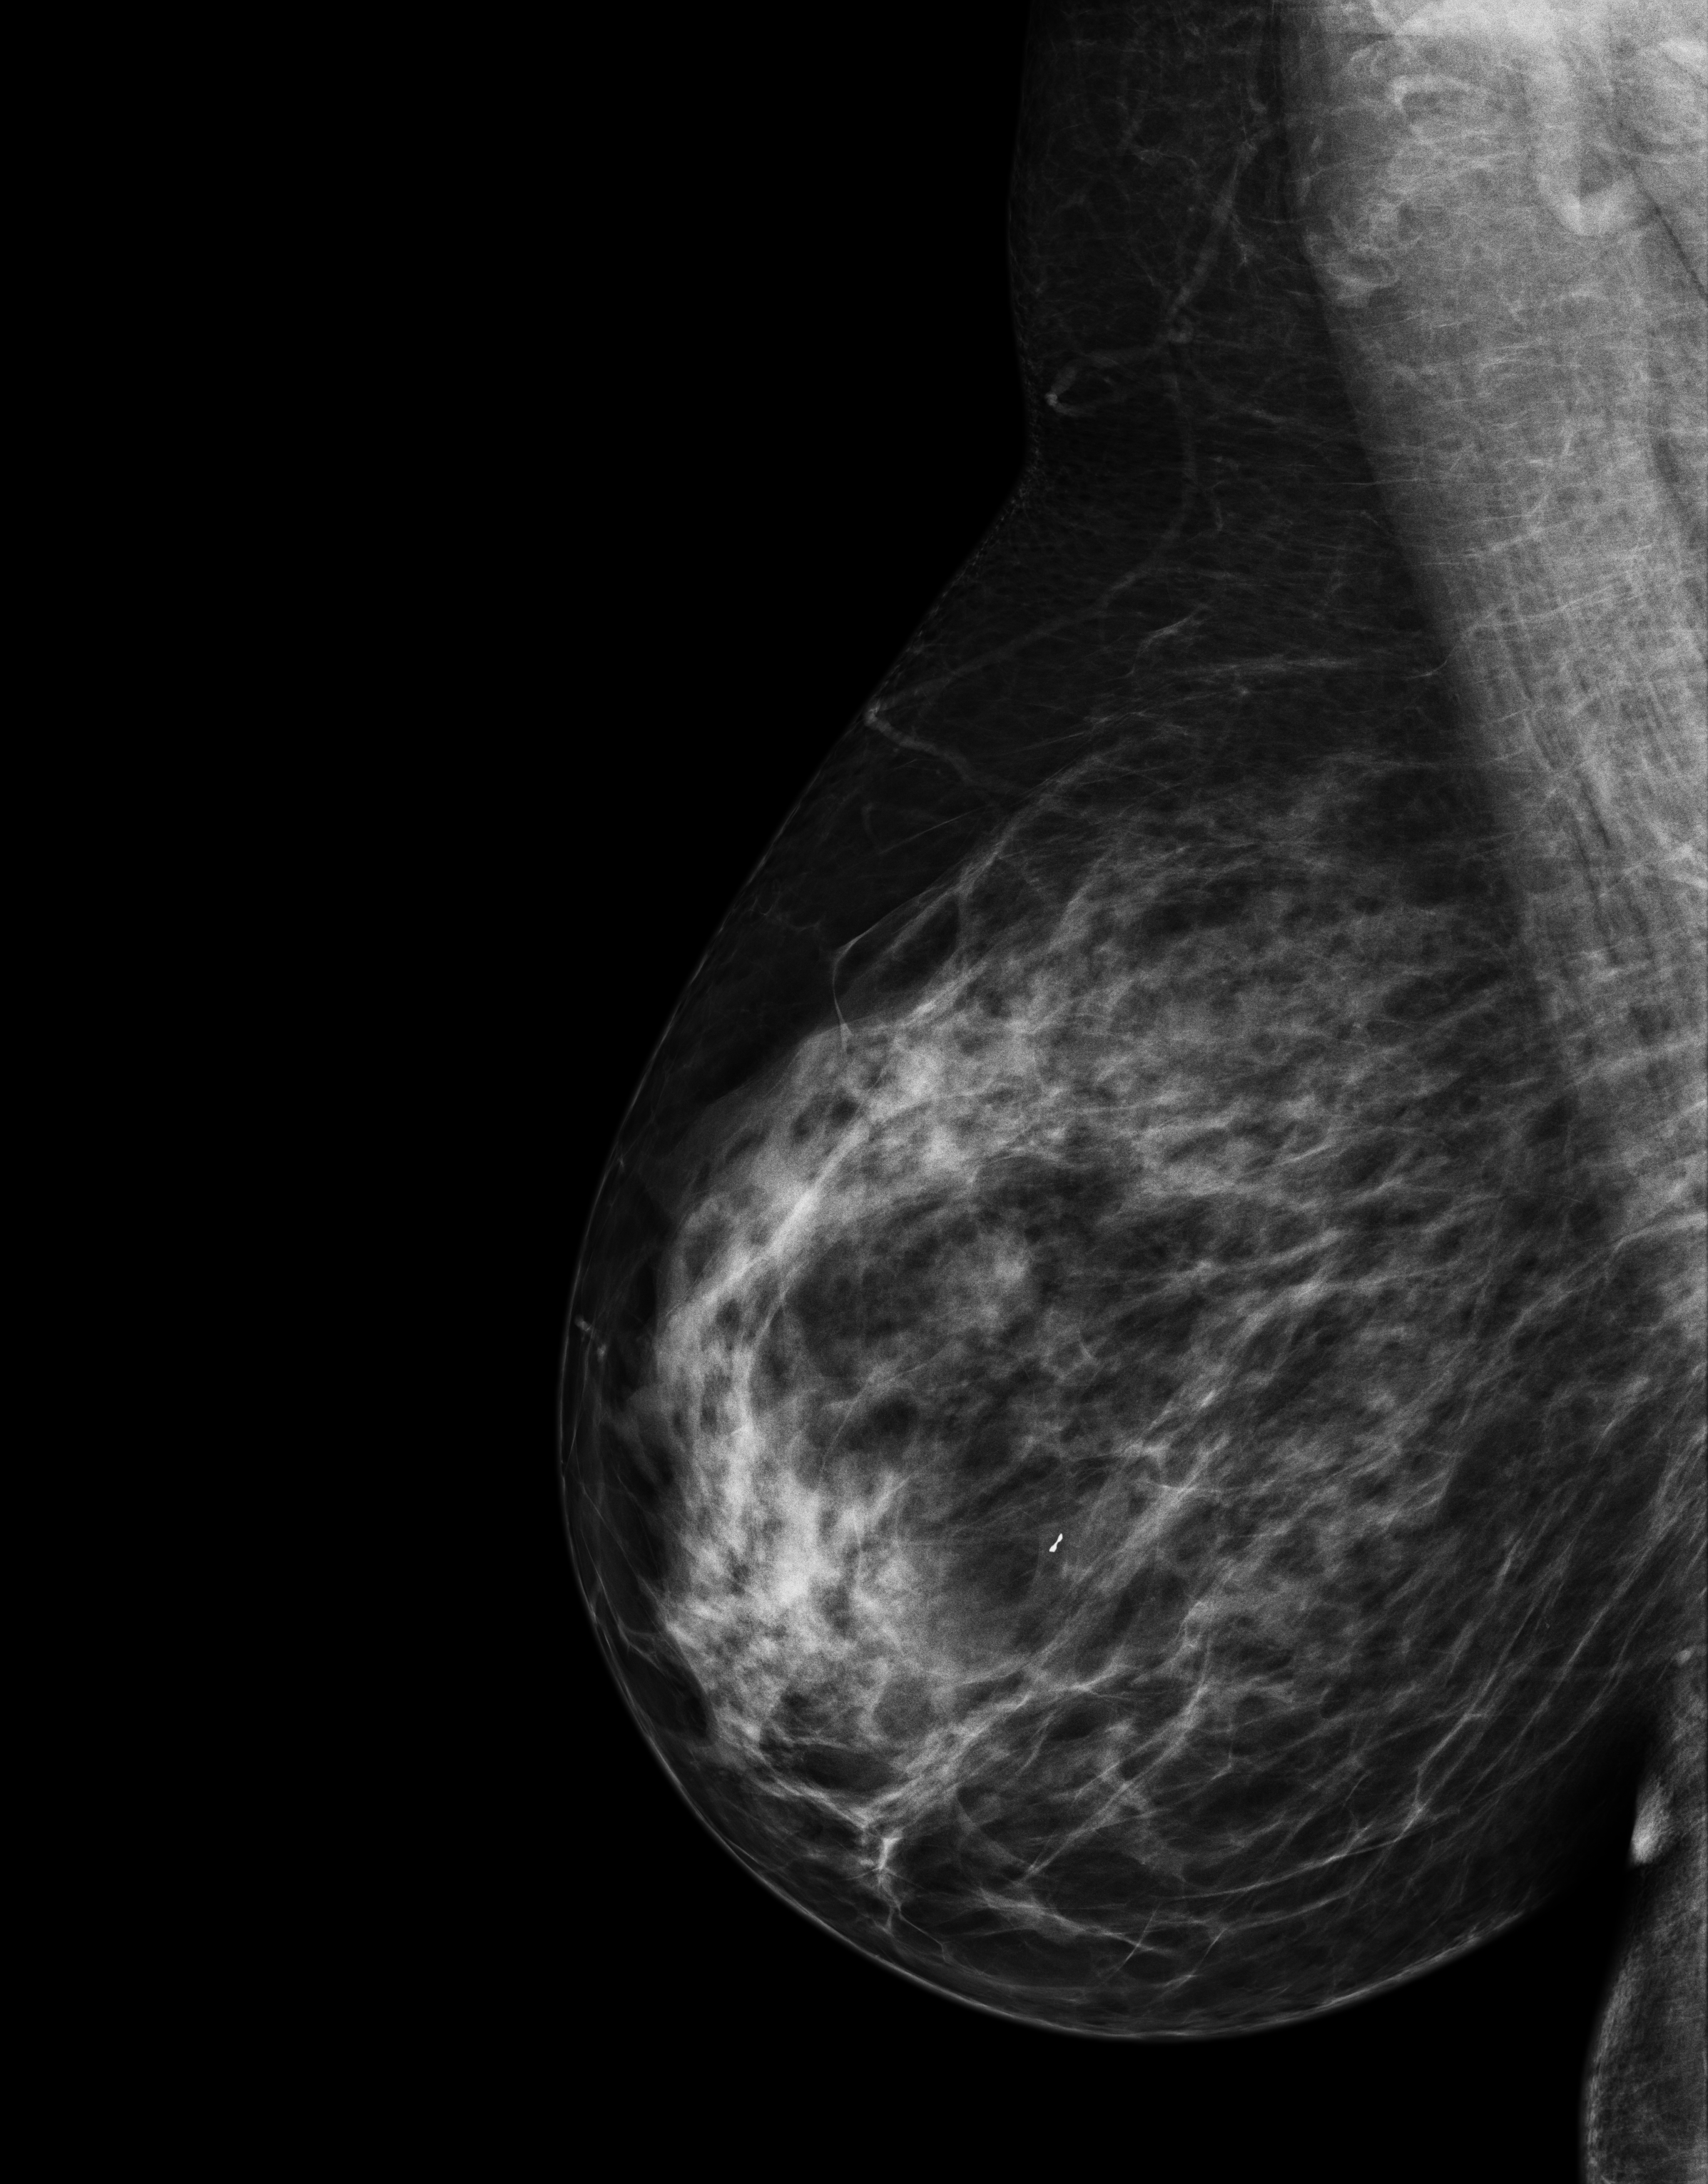
Annual screening mammography examination; system: Senographe Essential ADS_56.21.3. Patient: female, 43 years.
Image type: full-field digital mammogram. Breast: right. Projection: MLO view.